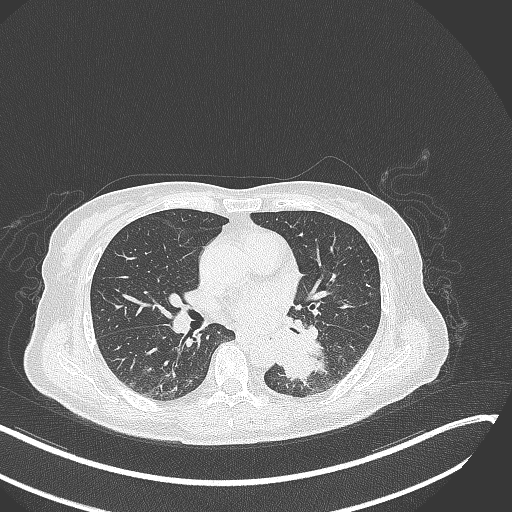
Chest CT, one axial slice. Slice 138 of 342 in the series (ordered by position). Reconstruction kernel B70f. Lung window (W 1500 / L -600 HU). 1 mm slice thickness. 512 × 512 image matrix. Patient: female, 64 years. From the clinical record (not read from this slice): clinical TNM (as recorded): T3 N1 M1; histopathological grade: G3.
Structures marked on this image (rectangle marked by the reading radiologist):
- lung tumour (recorded histology: small cell carcinoma): bounding box (x1, y1, x2, y2) in pixels: (268, 330, 330, 386)